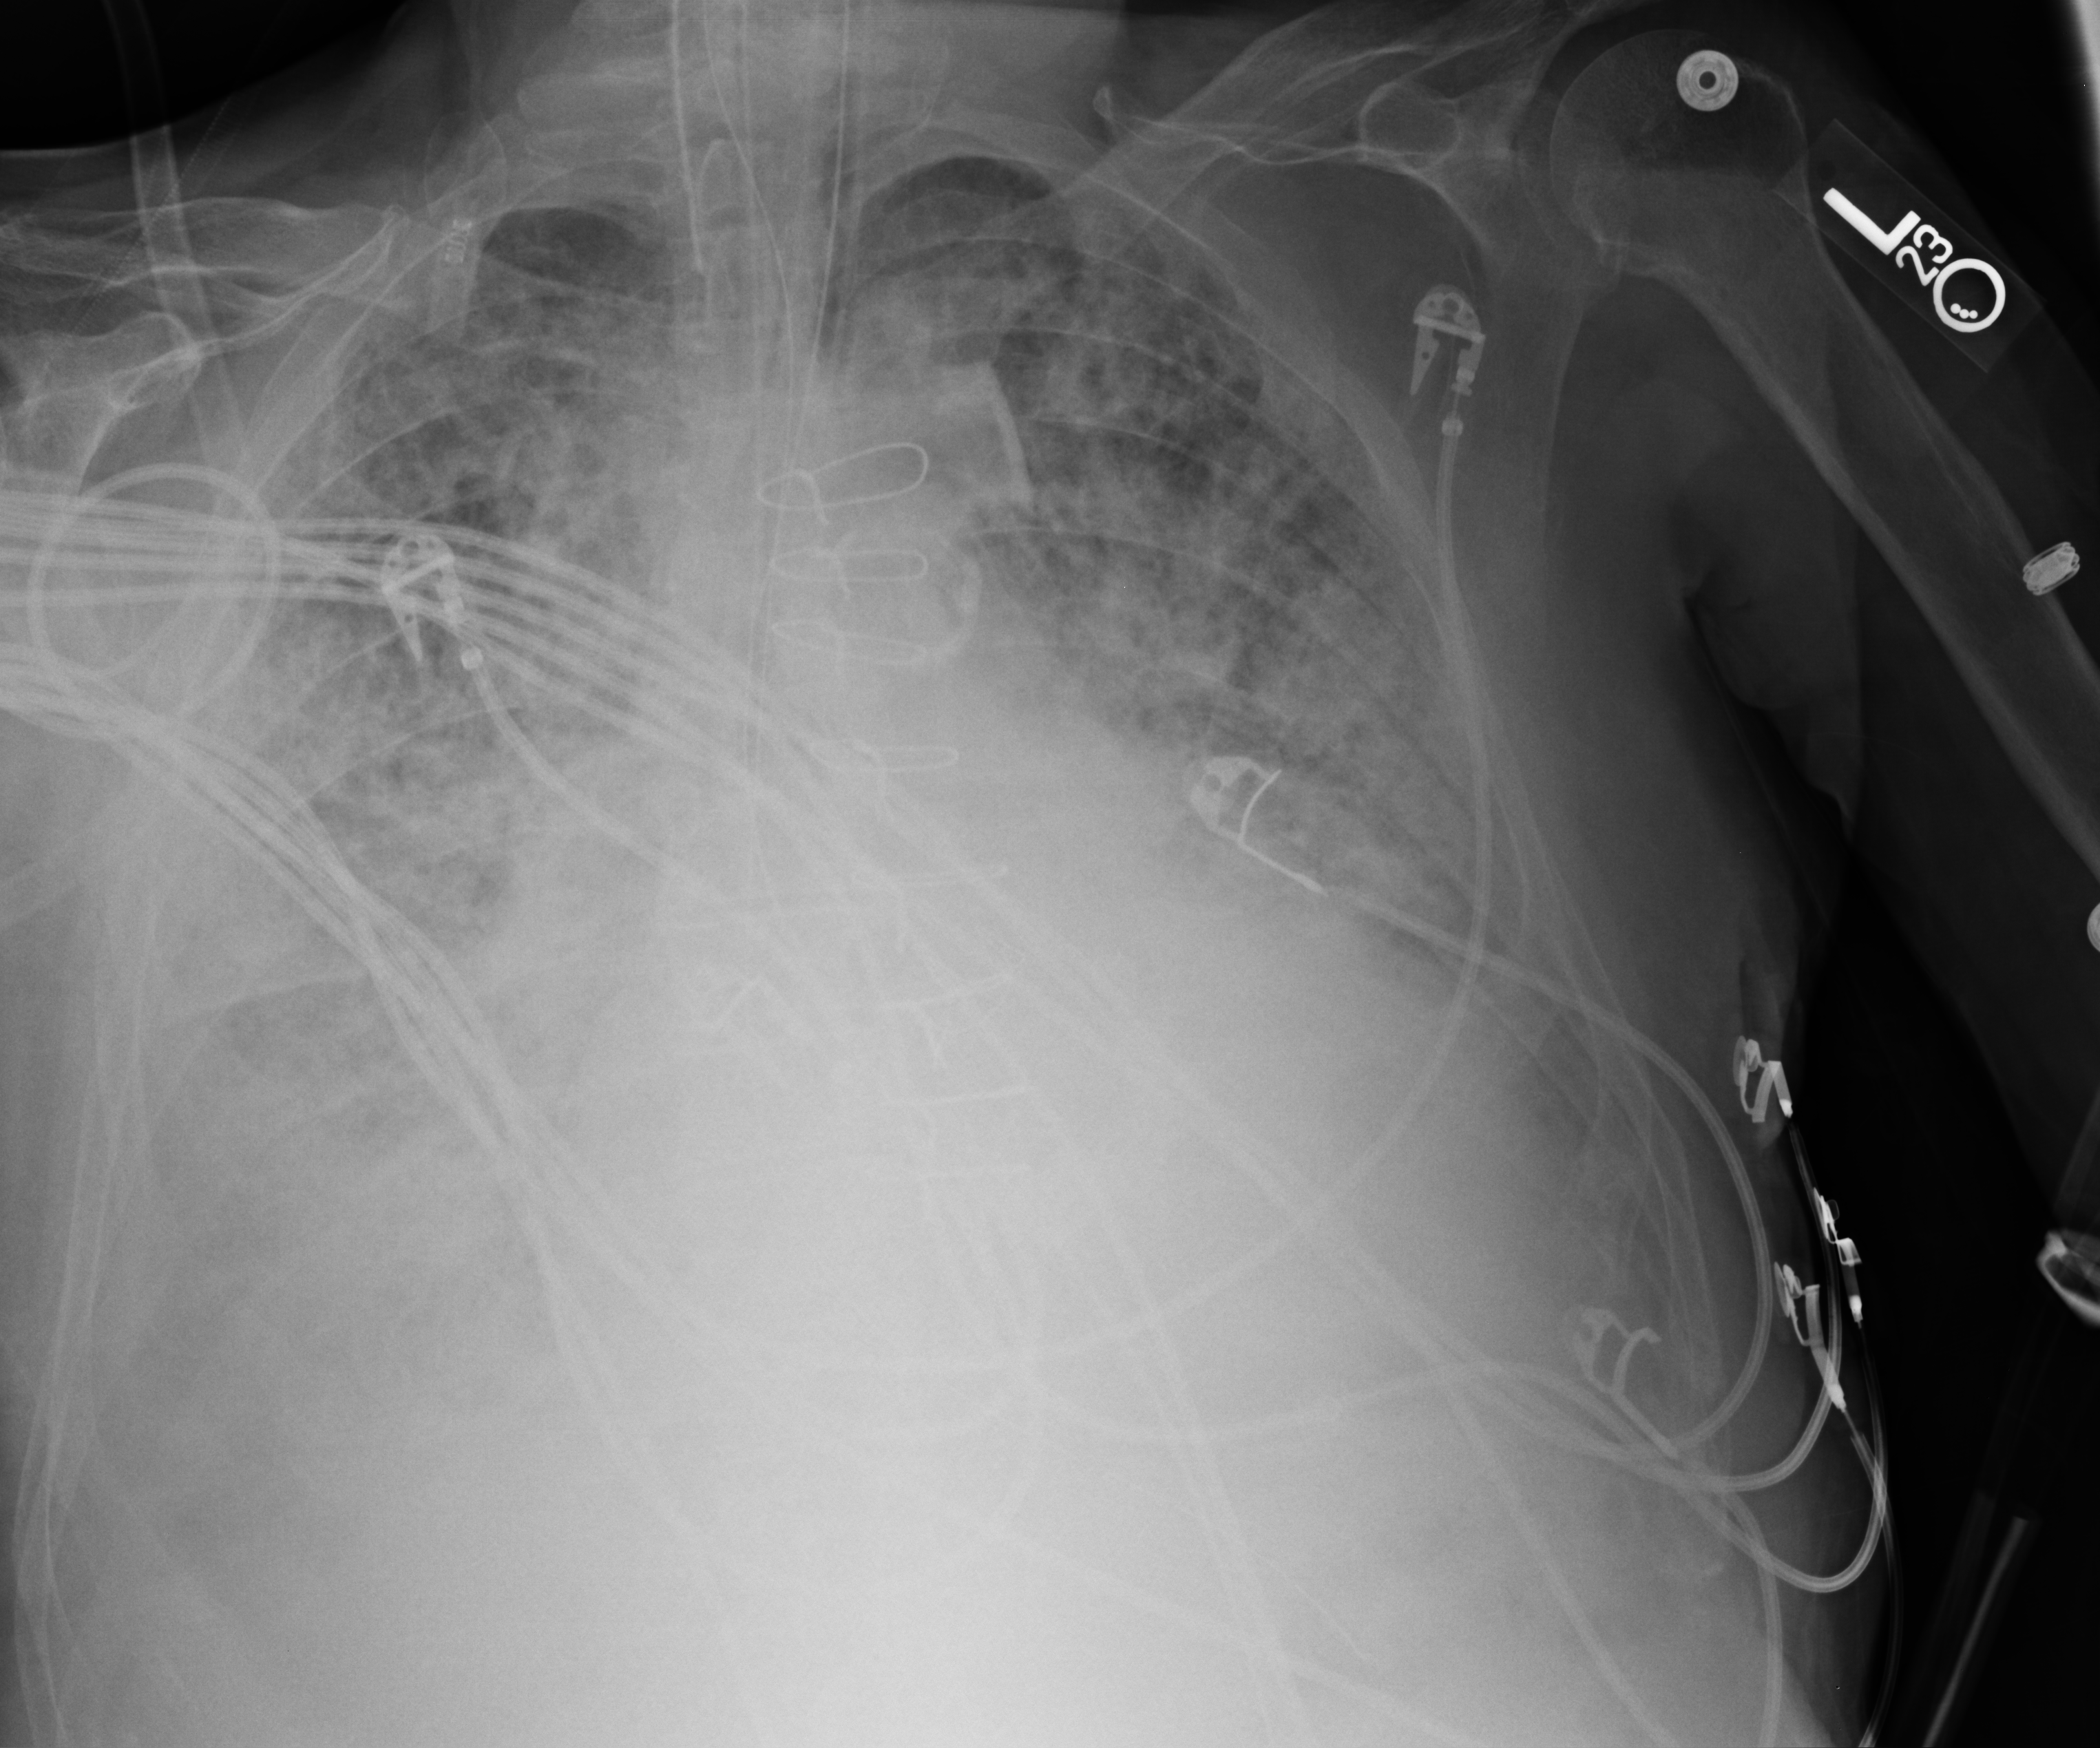
Bedside chest radiograph (computed radiography). Male patient hospitalised with COVID-19, age 75–90 years.
Hospital-stay facts (about this admission, not read from this image; timing relative to this image not recorded): admitted to intensive care during this hospital stay: yes.